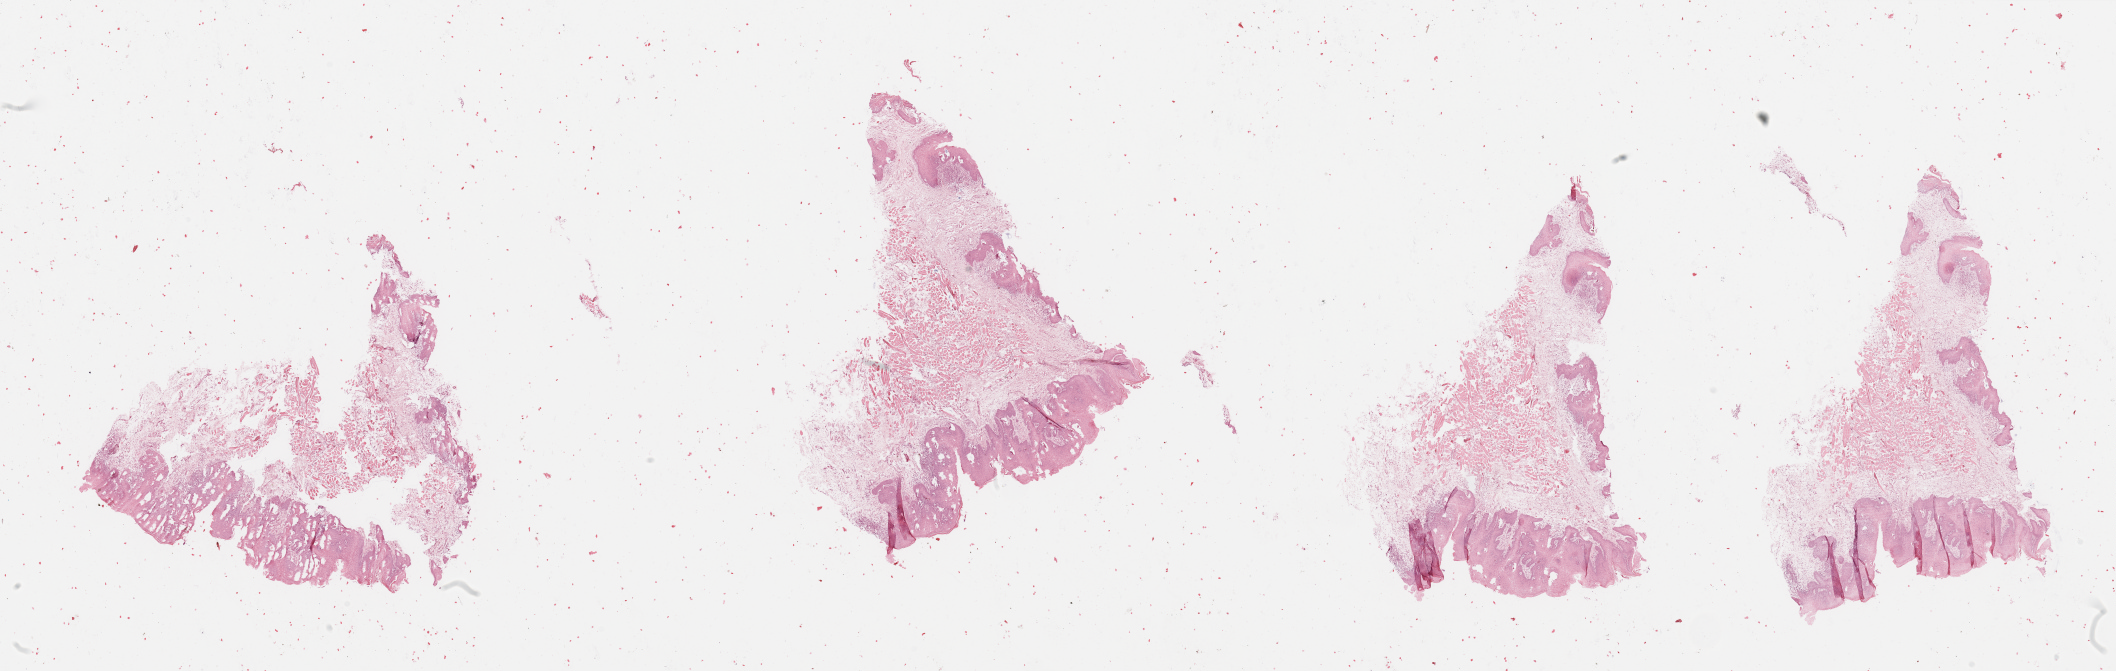
H&E whole-slide image, whole scanned area (about 33.5 x 10.6 mm, acquisition: 20x scan) shown as a low-resolution overview; normal (non-tumour) tissue sample, sampled site: floor of mouth. Patient: male, age 59 years.
This section: normal (non-tumour) tissue from the same patient. Patient diagnosis: Squamous cell carcinoma, NOS (floor of mouth, NOS).